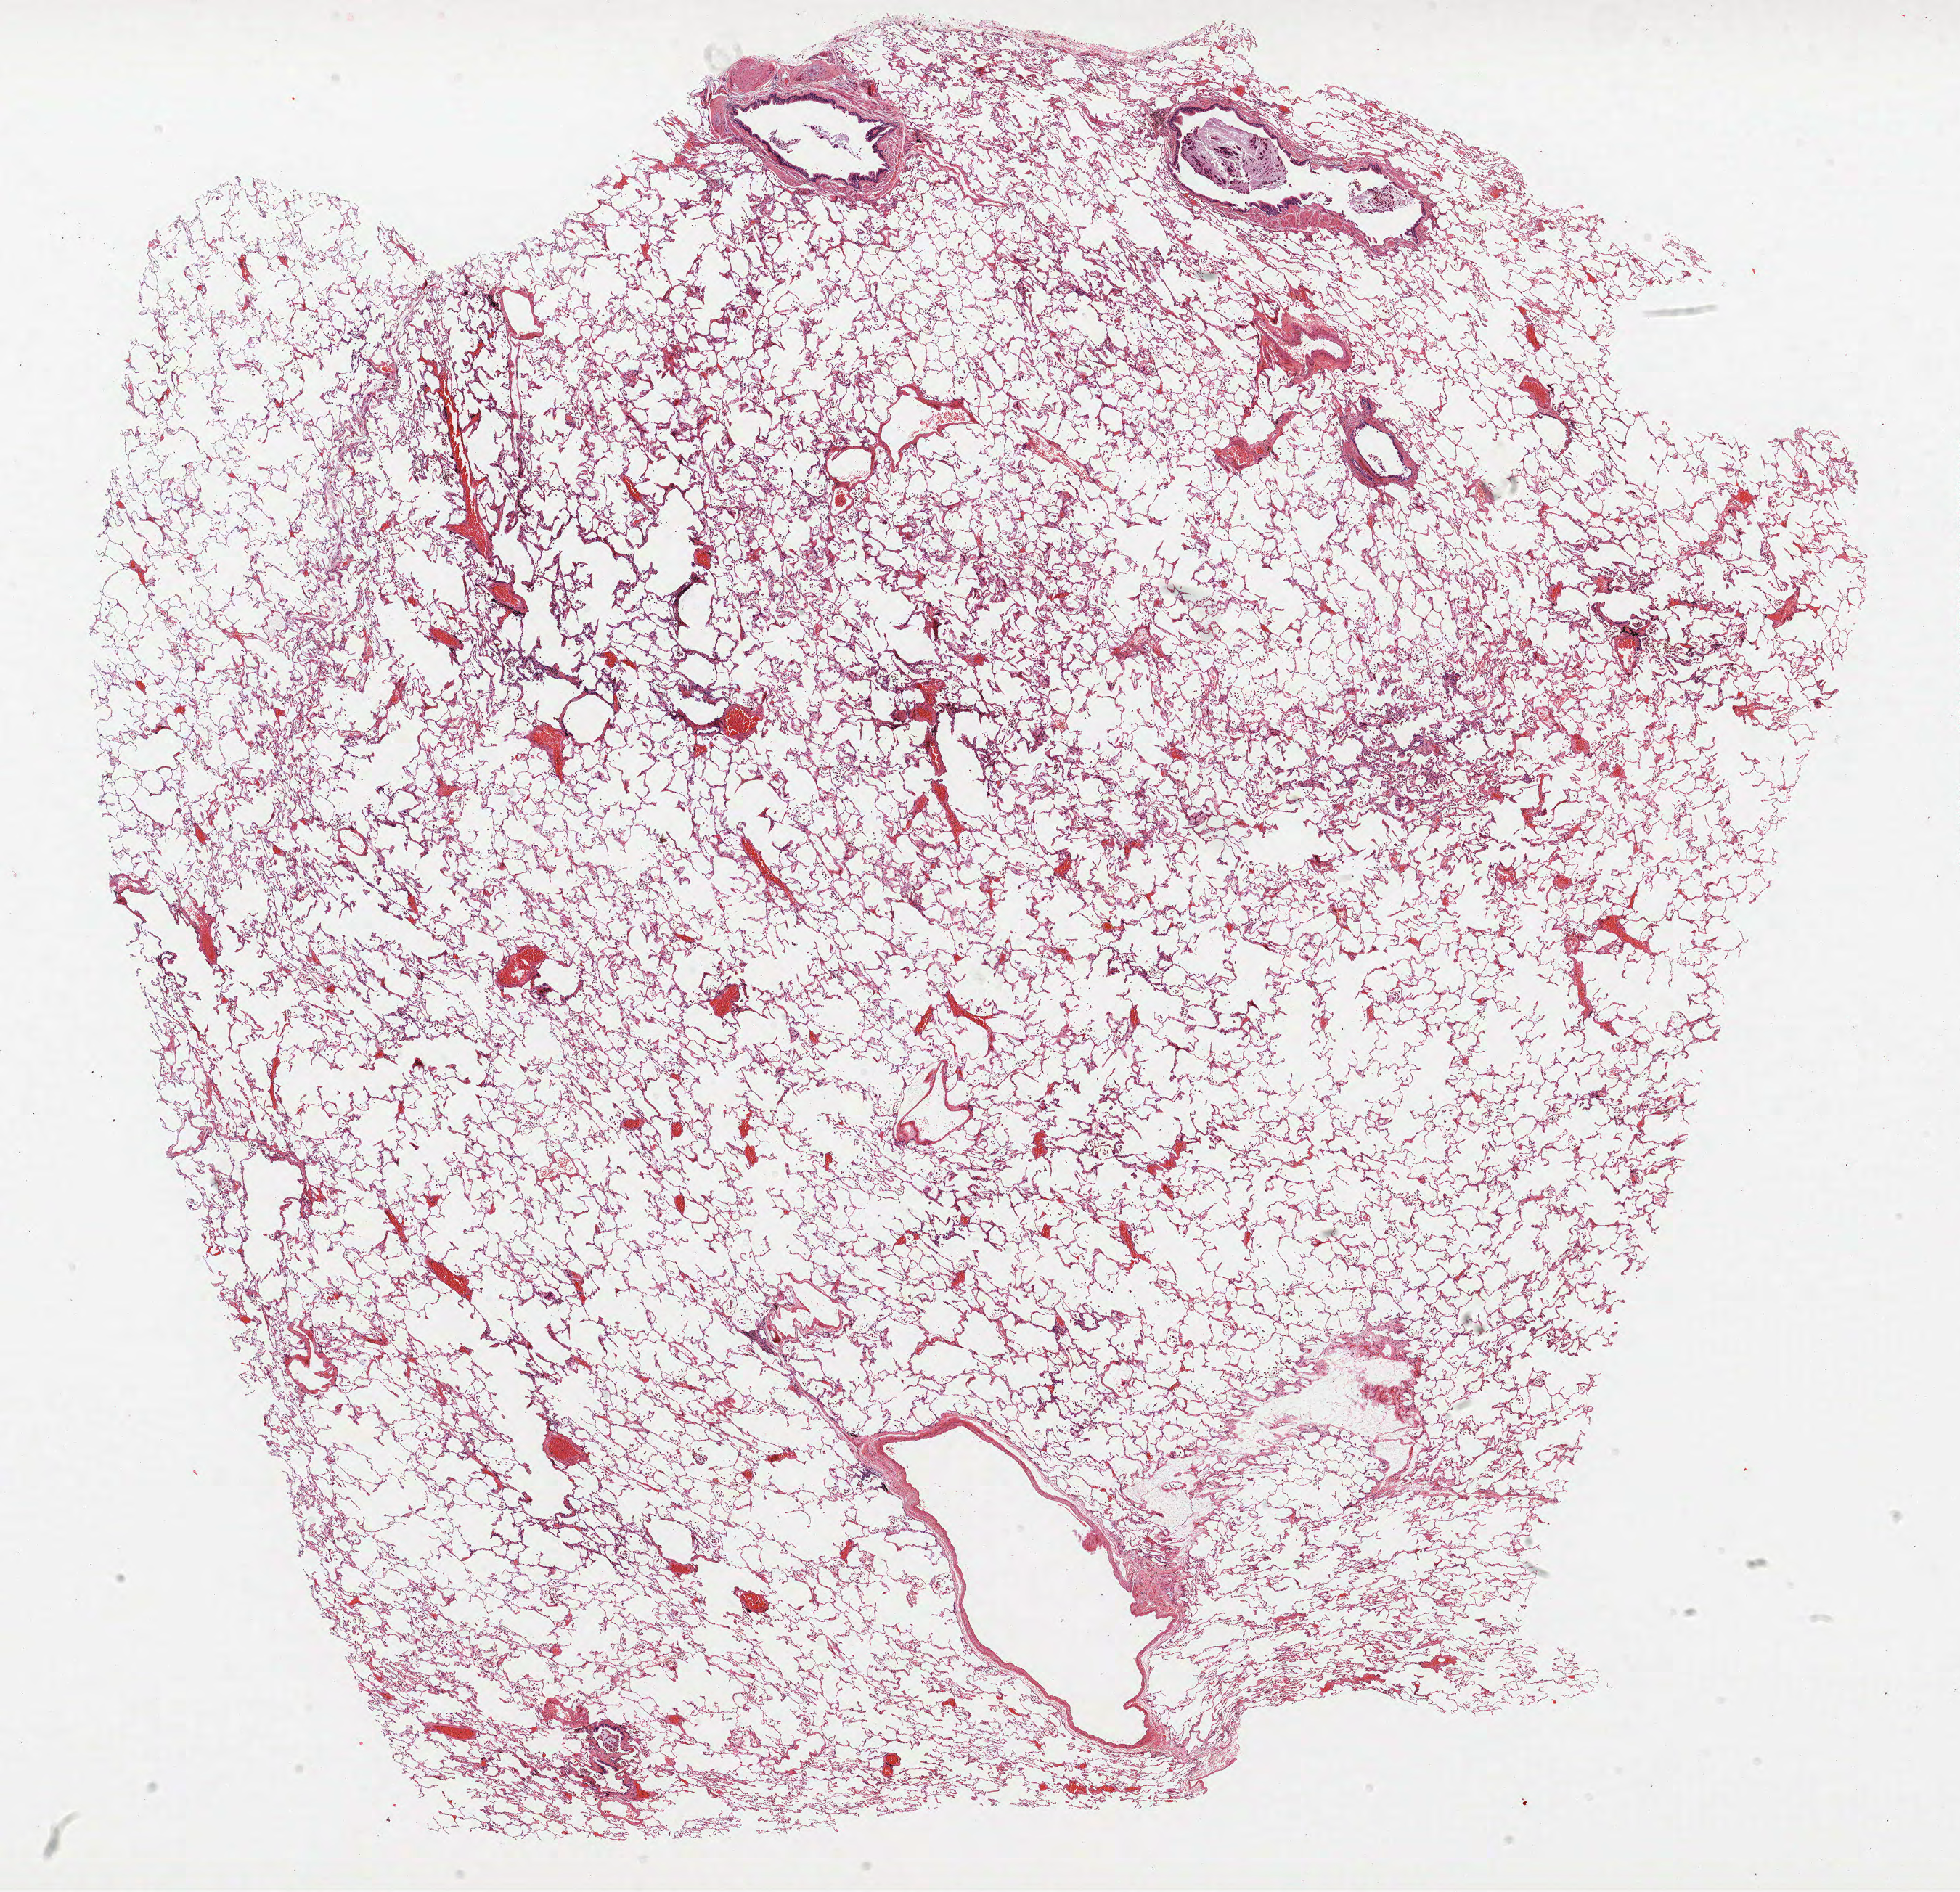
H&E whole-slide image — whole scanned area (about 21.6 x 20.9 mm, acquisition: 40x scan) shown as a low-resolution overview, FFPE section, lung. Male patient, aged 62 at enrolment. Current smoker at enrolment. Grade: well differentiated (G1).
Primary tumour location (clinical record): left upper lobe. Participant's lung-cancer diagnosis: Adenocarcinoma, NOS (ICD-O-3 8140/3). Stage (AJCC 6th edition): IB. Tumour size (pathology): 17 mm.